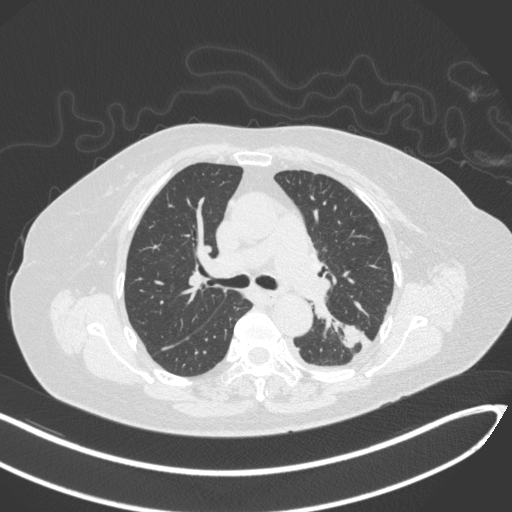
Chest CT, one axial slice. Position 200 of 270 along the scan axis. Reconstruction kernel B31f. Lung window (W 1500 / L -600 HU). 1 mm slice thickness. 512 × 512 image matrix, field of view 400 × 400 mm. Patient: female, 76 years. Case-level facts recorded for this patient, not image findings: clinical TNM (as recorded): T1c N0 M0.
Annotated regions visible in this slice (bounding box drawn by a radiologist):
- lung tumour (recorded histology: adenocarcinoma): box from (x=338, y=319) to (x=365, y=351) px